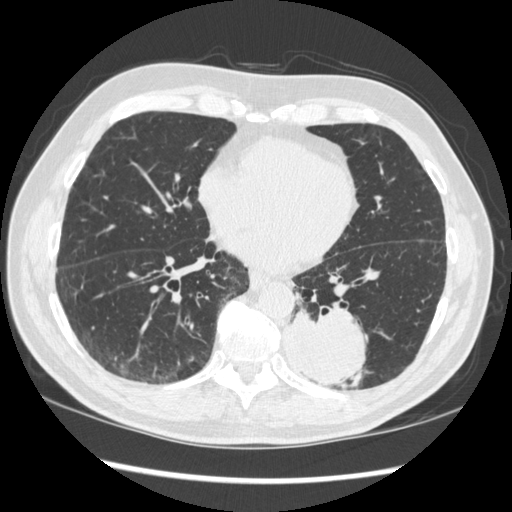
Chest CT (low-dose screening protocol), one axial image, baseline screening round, lung window (W 1500 / L -600 HU), 1.25 mm slice thickness, standard (soft-tissue) reconstruction kernel (STANDARD), slice 128 of 348 in the series. Male, age 72 years at enrolment. Current smoker at enrolment.
Expert-annotated lung lesion, box from (x=272, y=298) to (x=376, y=387) px. The screening reader recorded 2 non-calcified nodules or masses ≥4 mm on this exam; which of them this box marks is not recorded. Later outcome: lung cancer diagnosed 37 days after this screen — squamous cell carcinoma, NOS, left lower lobe, stage IIIA (AJCC 6th edition), 60 mm at pathology.